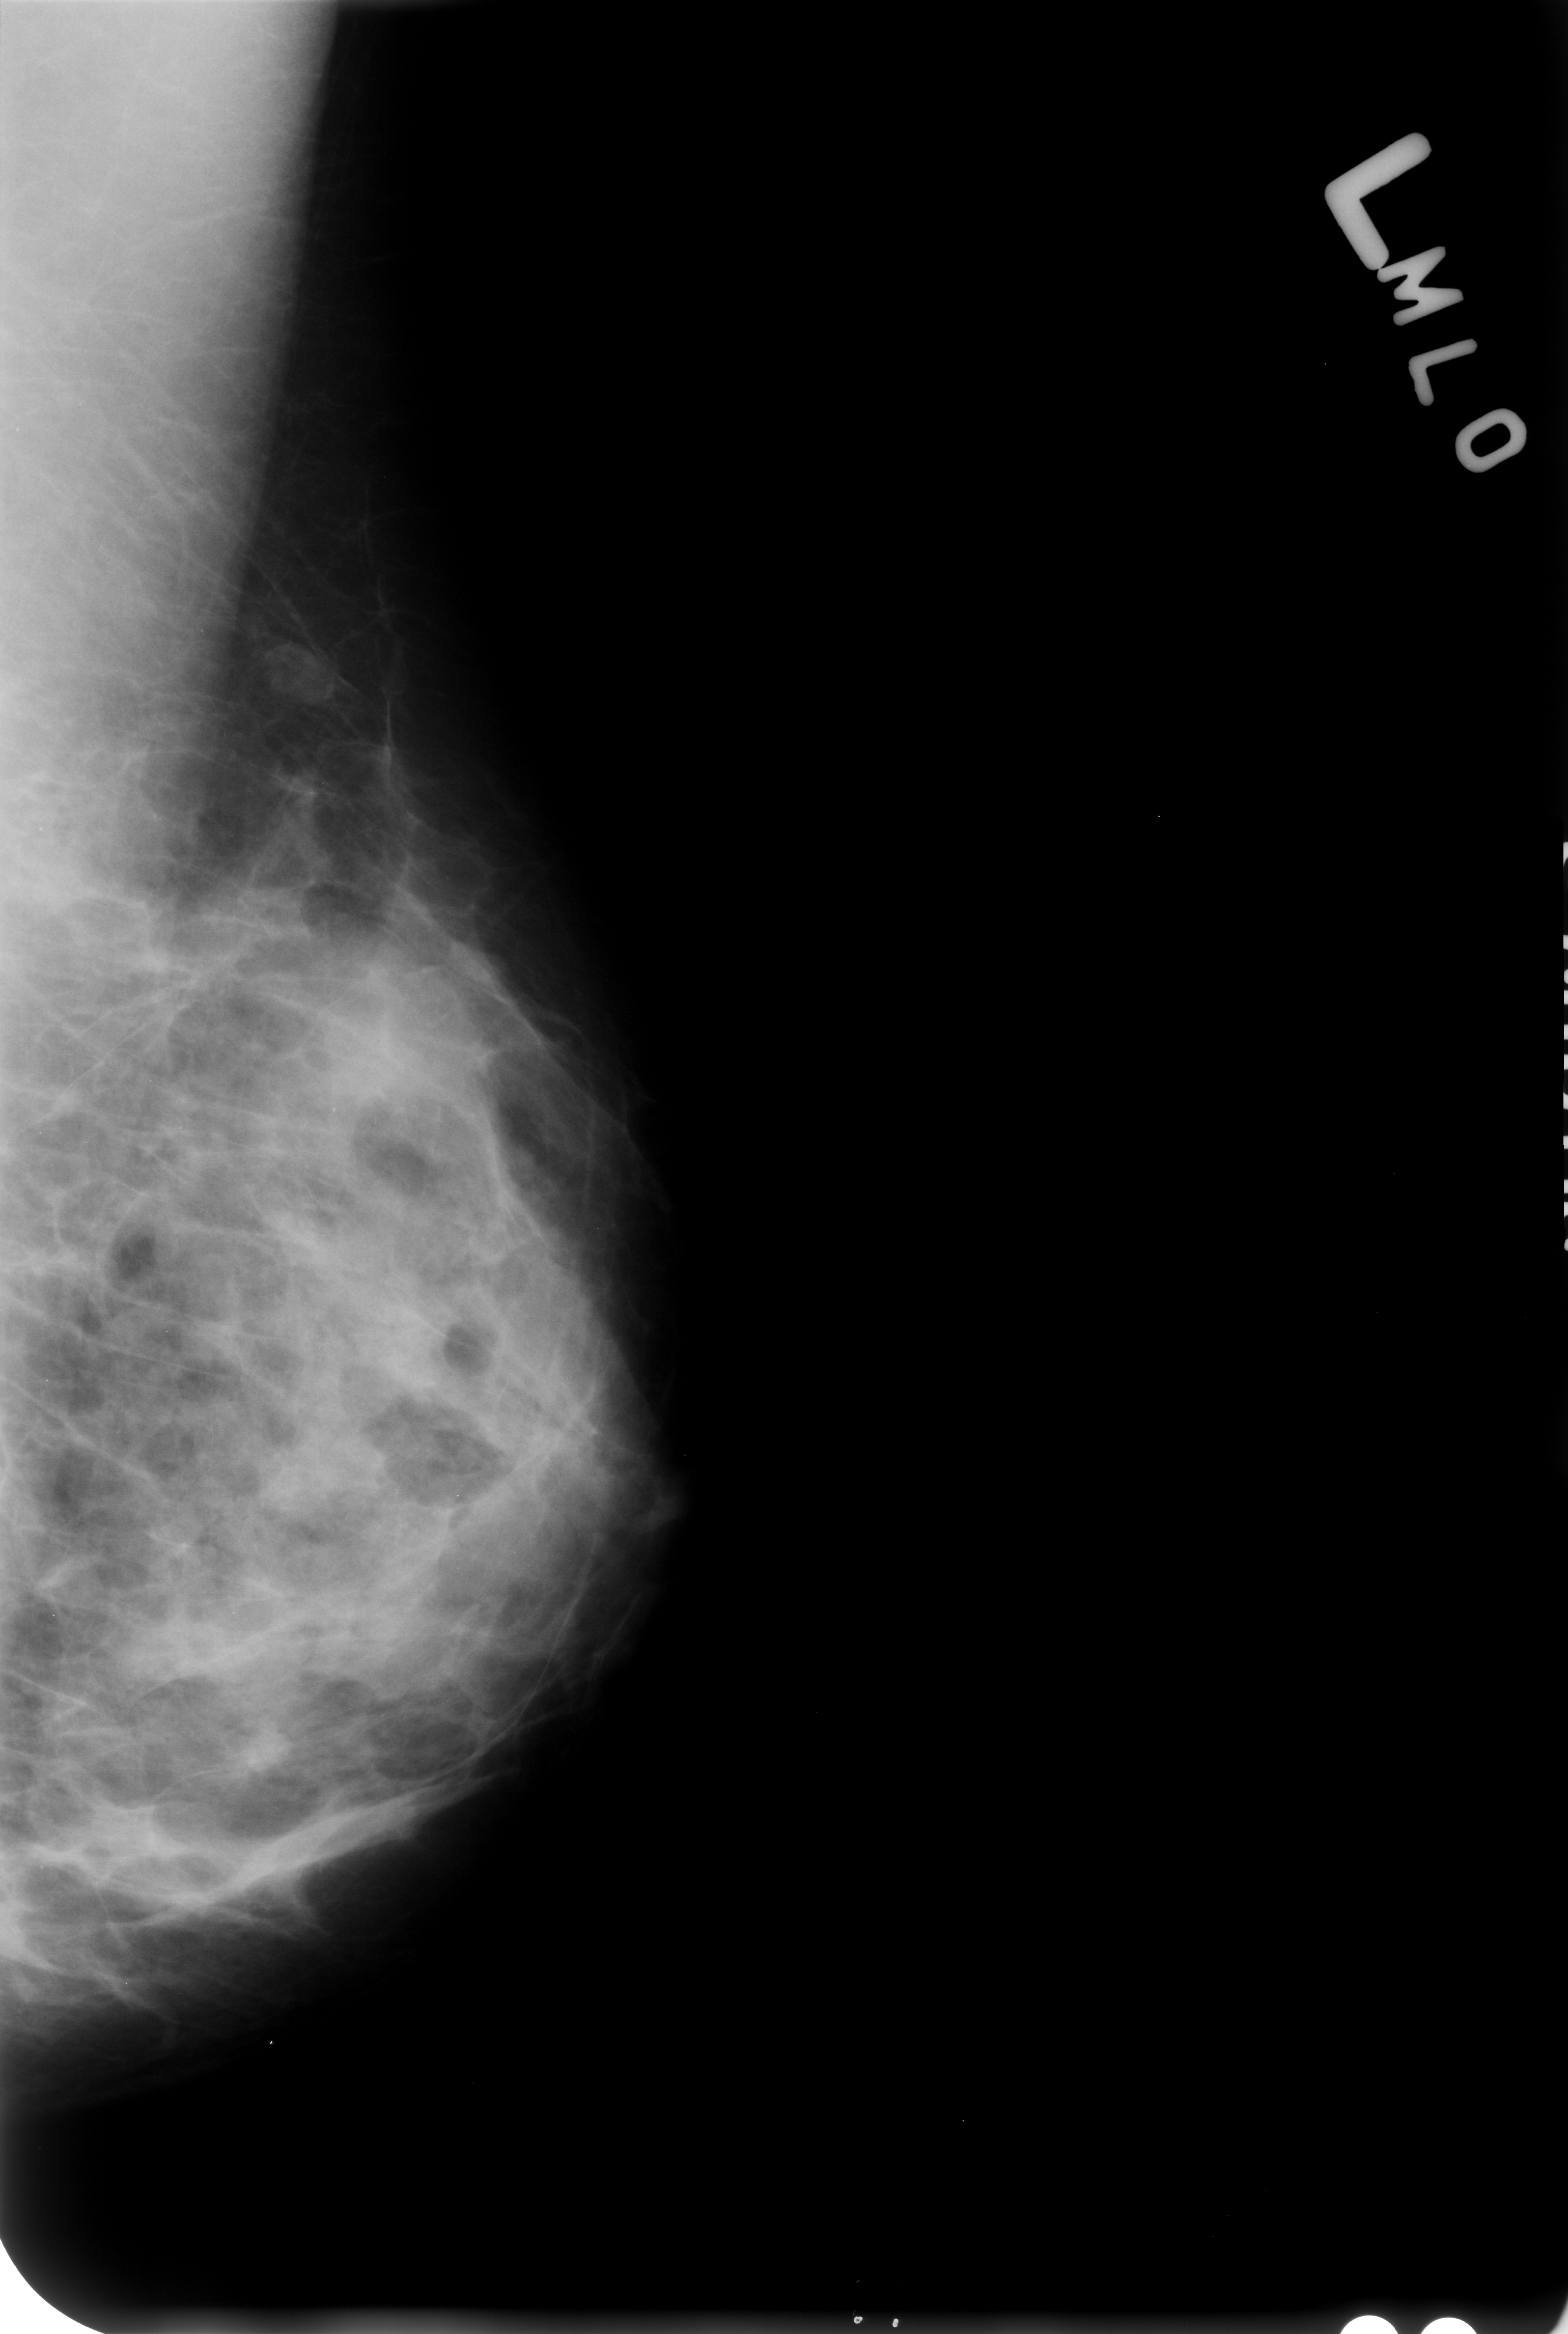
Digitized screen-film mammogram, left breast, MLO view, BI-RADS breast density category 3 (scale 1–4).
Marked findings (only marked abnormalities are described; nothing is implied about the rest of the image): calcifications, morphology punctate; BI-RADS assessment category 2; benign without callback (not worked up further).